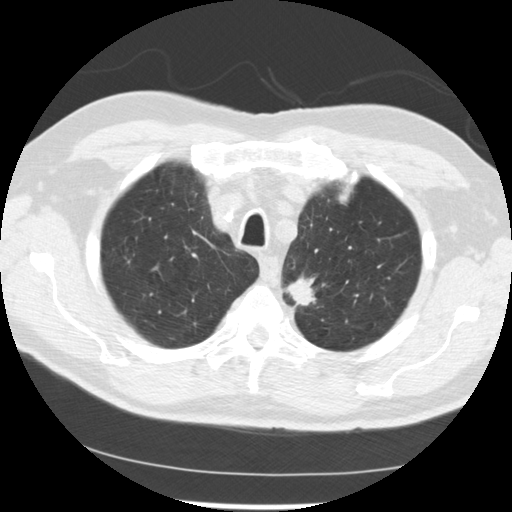
Low-dose screening chest CT, one axial slice. Slice 204 of 249 in the series (ordered by position). Reconstruction kernel STANDARD. 120 kVp. Lung window (W 1500 / L -600 HU). 512 × 512 image matrix, field of view 341 × 341 mm.
Outlined on this slice (manually delineated by an expert):
- lesion 2 (tumor, upper lobe of left lung): bounding box [x1, y1, x2, y2] px = [287, 277, 316, 306]